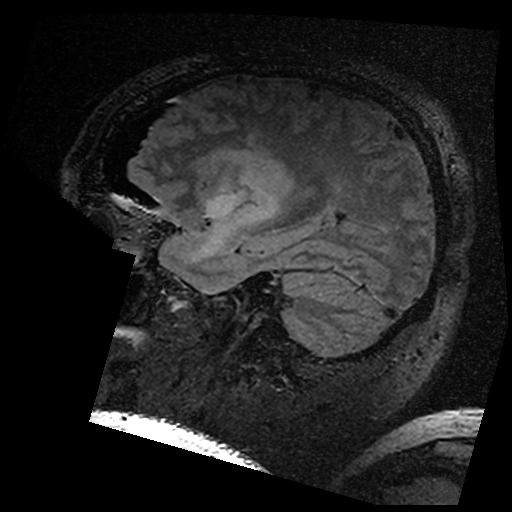
Brain MRI from a brain-tumour surgery series, one sagittal slice. Position 119 of 176 along the scan axis. T2 FLAIR. 1 mm slice thickness. 512 × 512 image matrix. Case-level facts recorded for this patient, not image findings: histopathology: Astrocytoma; WHO grade: 3; IDH mutation: yes.
Outlined on this slice (manually delineated by an expert):
- residual tumour: bounding box [x1, y1, x2, y2] px = [202, 146, 292, 196]